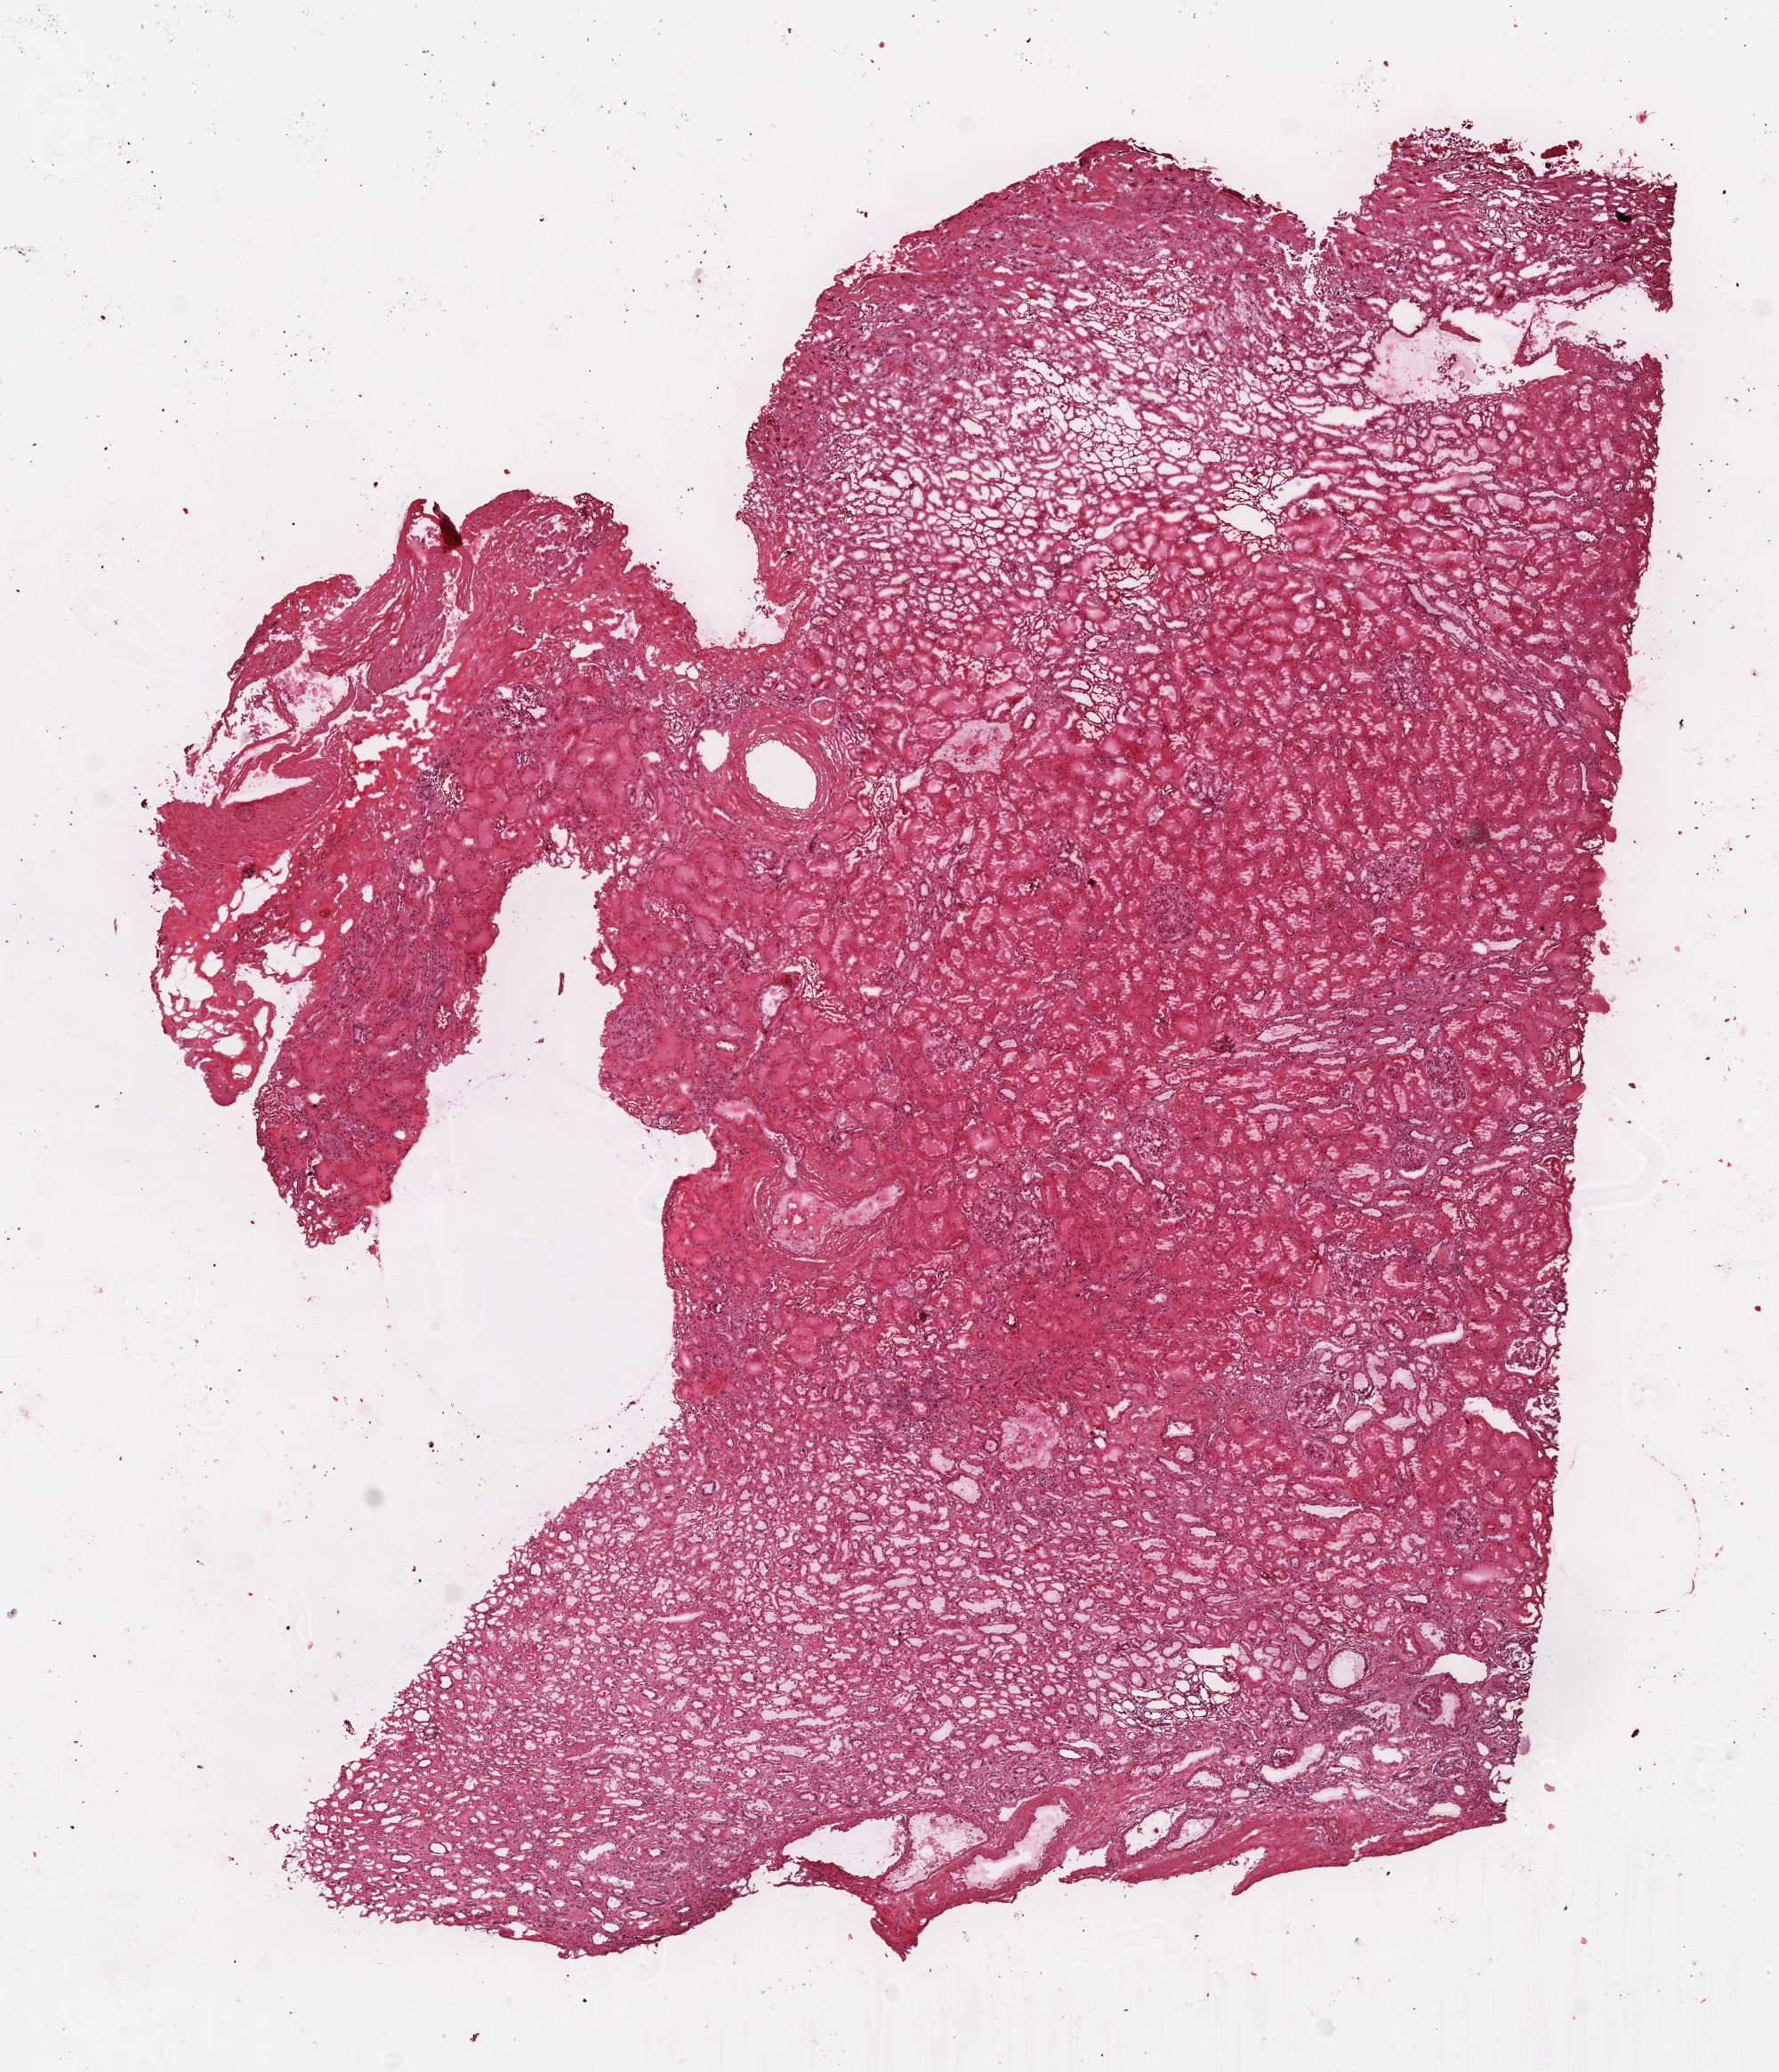
H&E whole-slide image — whole scanned area (about 8.0 x 9.3 mm) shown as a low-resolution overview, frozen section from the top of the tissue portion, solid tissue normal (non-tumour tissue) sample from the kidney. Female, age 68 years at initial diagnosis.
- this section: solid tissue normal sample (biorepository sample class)
- patient diagnosis: Clear cell adenocarcinoma, NOS